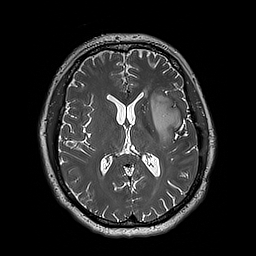
Brain MRI from a brain-tumour surgery series, one axial slice. Position 97 of 192 along the scan axis. 256 × 256 image matrix, field of view 250 × 250 mm. Case-level facts recorded for this patient, not image findings: histopathology: Astrocytoma; WHO grade: 3; IDH mutation: yes; tumour location: Left Insular.
Structures marked on this image (manually delineated by an expert):
- tumour: box from (x=150, y=94) to (x=183, y=143) px